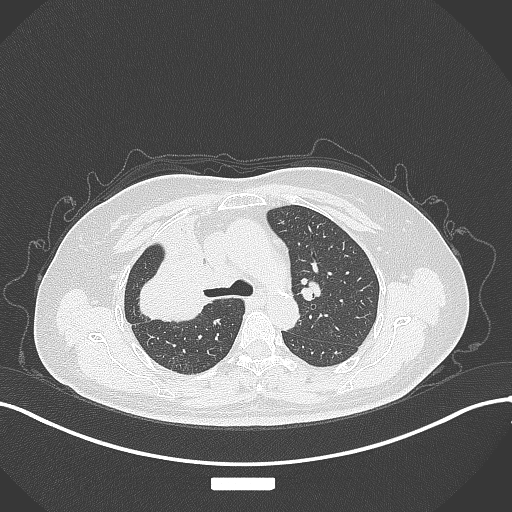
Chest CT, one axial slice; slice 215 of 309 in the series (ordered by position); 120 kVp; lung window (W 1500 / L -600 HU); 1 mm slice thickness; 512 × 512 image matrix, field of view 400 × 400 mm. Female patient, age 60 years. From the clinical record (not read from this slice): clinical TNM (as recorded): T3 N1 M1.
Outlined on this slice (rectangle marked by the reading radiologist):
- lung tumour (recorded histology: adenocarcinoma): bounding box (x1, y1, x2, y2) in pixels: (133, 243, 212, 324)